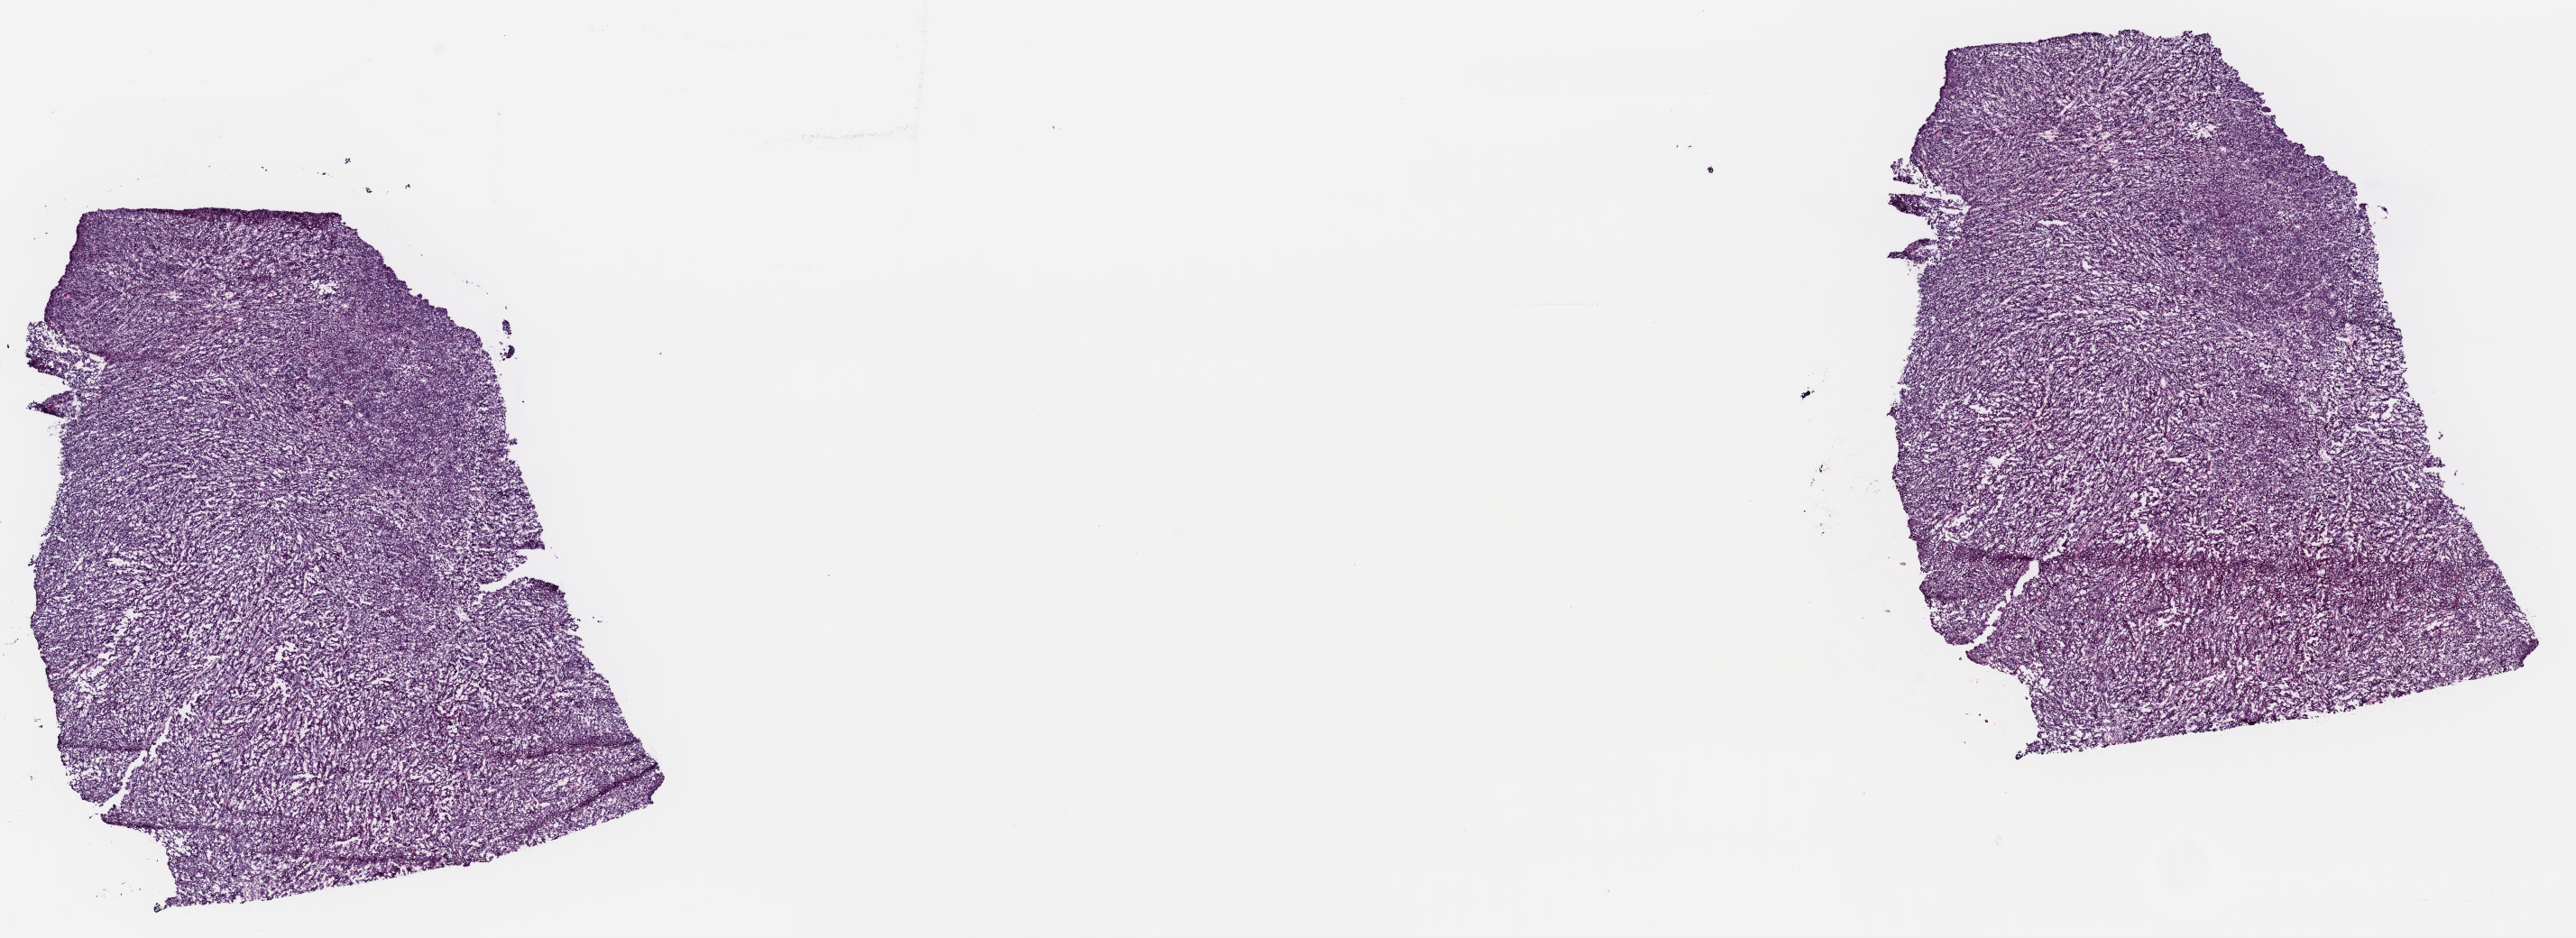
Whole-slide histology image, Hematoxylin and eosin (H&E) stained, whole scanned area (about 22.6 x 8.2 mm, acquisition: 40x scan) shown as a low-resolution overview, frozen section from the top of the tissue portion, metastatic tumour sample, sampled site: lymph nodes of head, face and neck. Male, age 82 years at initial diagnosis. Slide review estimates, as recorded: tumour cells 100%, tumour nuclei 96%, normal cells 0%, stromal cells 0%, necrosis 0%. Infiltration values recorded for this section: lymphocyte infiltration 0%, monocyte infiltration 0%, neutrophil infiltration 0%.
This section: metastatic tumour tissue. Patient diagnosis: Malignant melanoma, NOS.